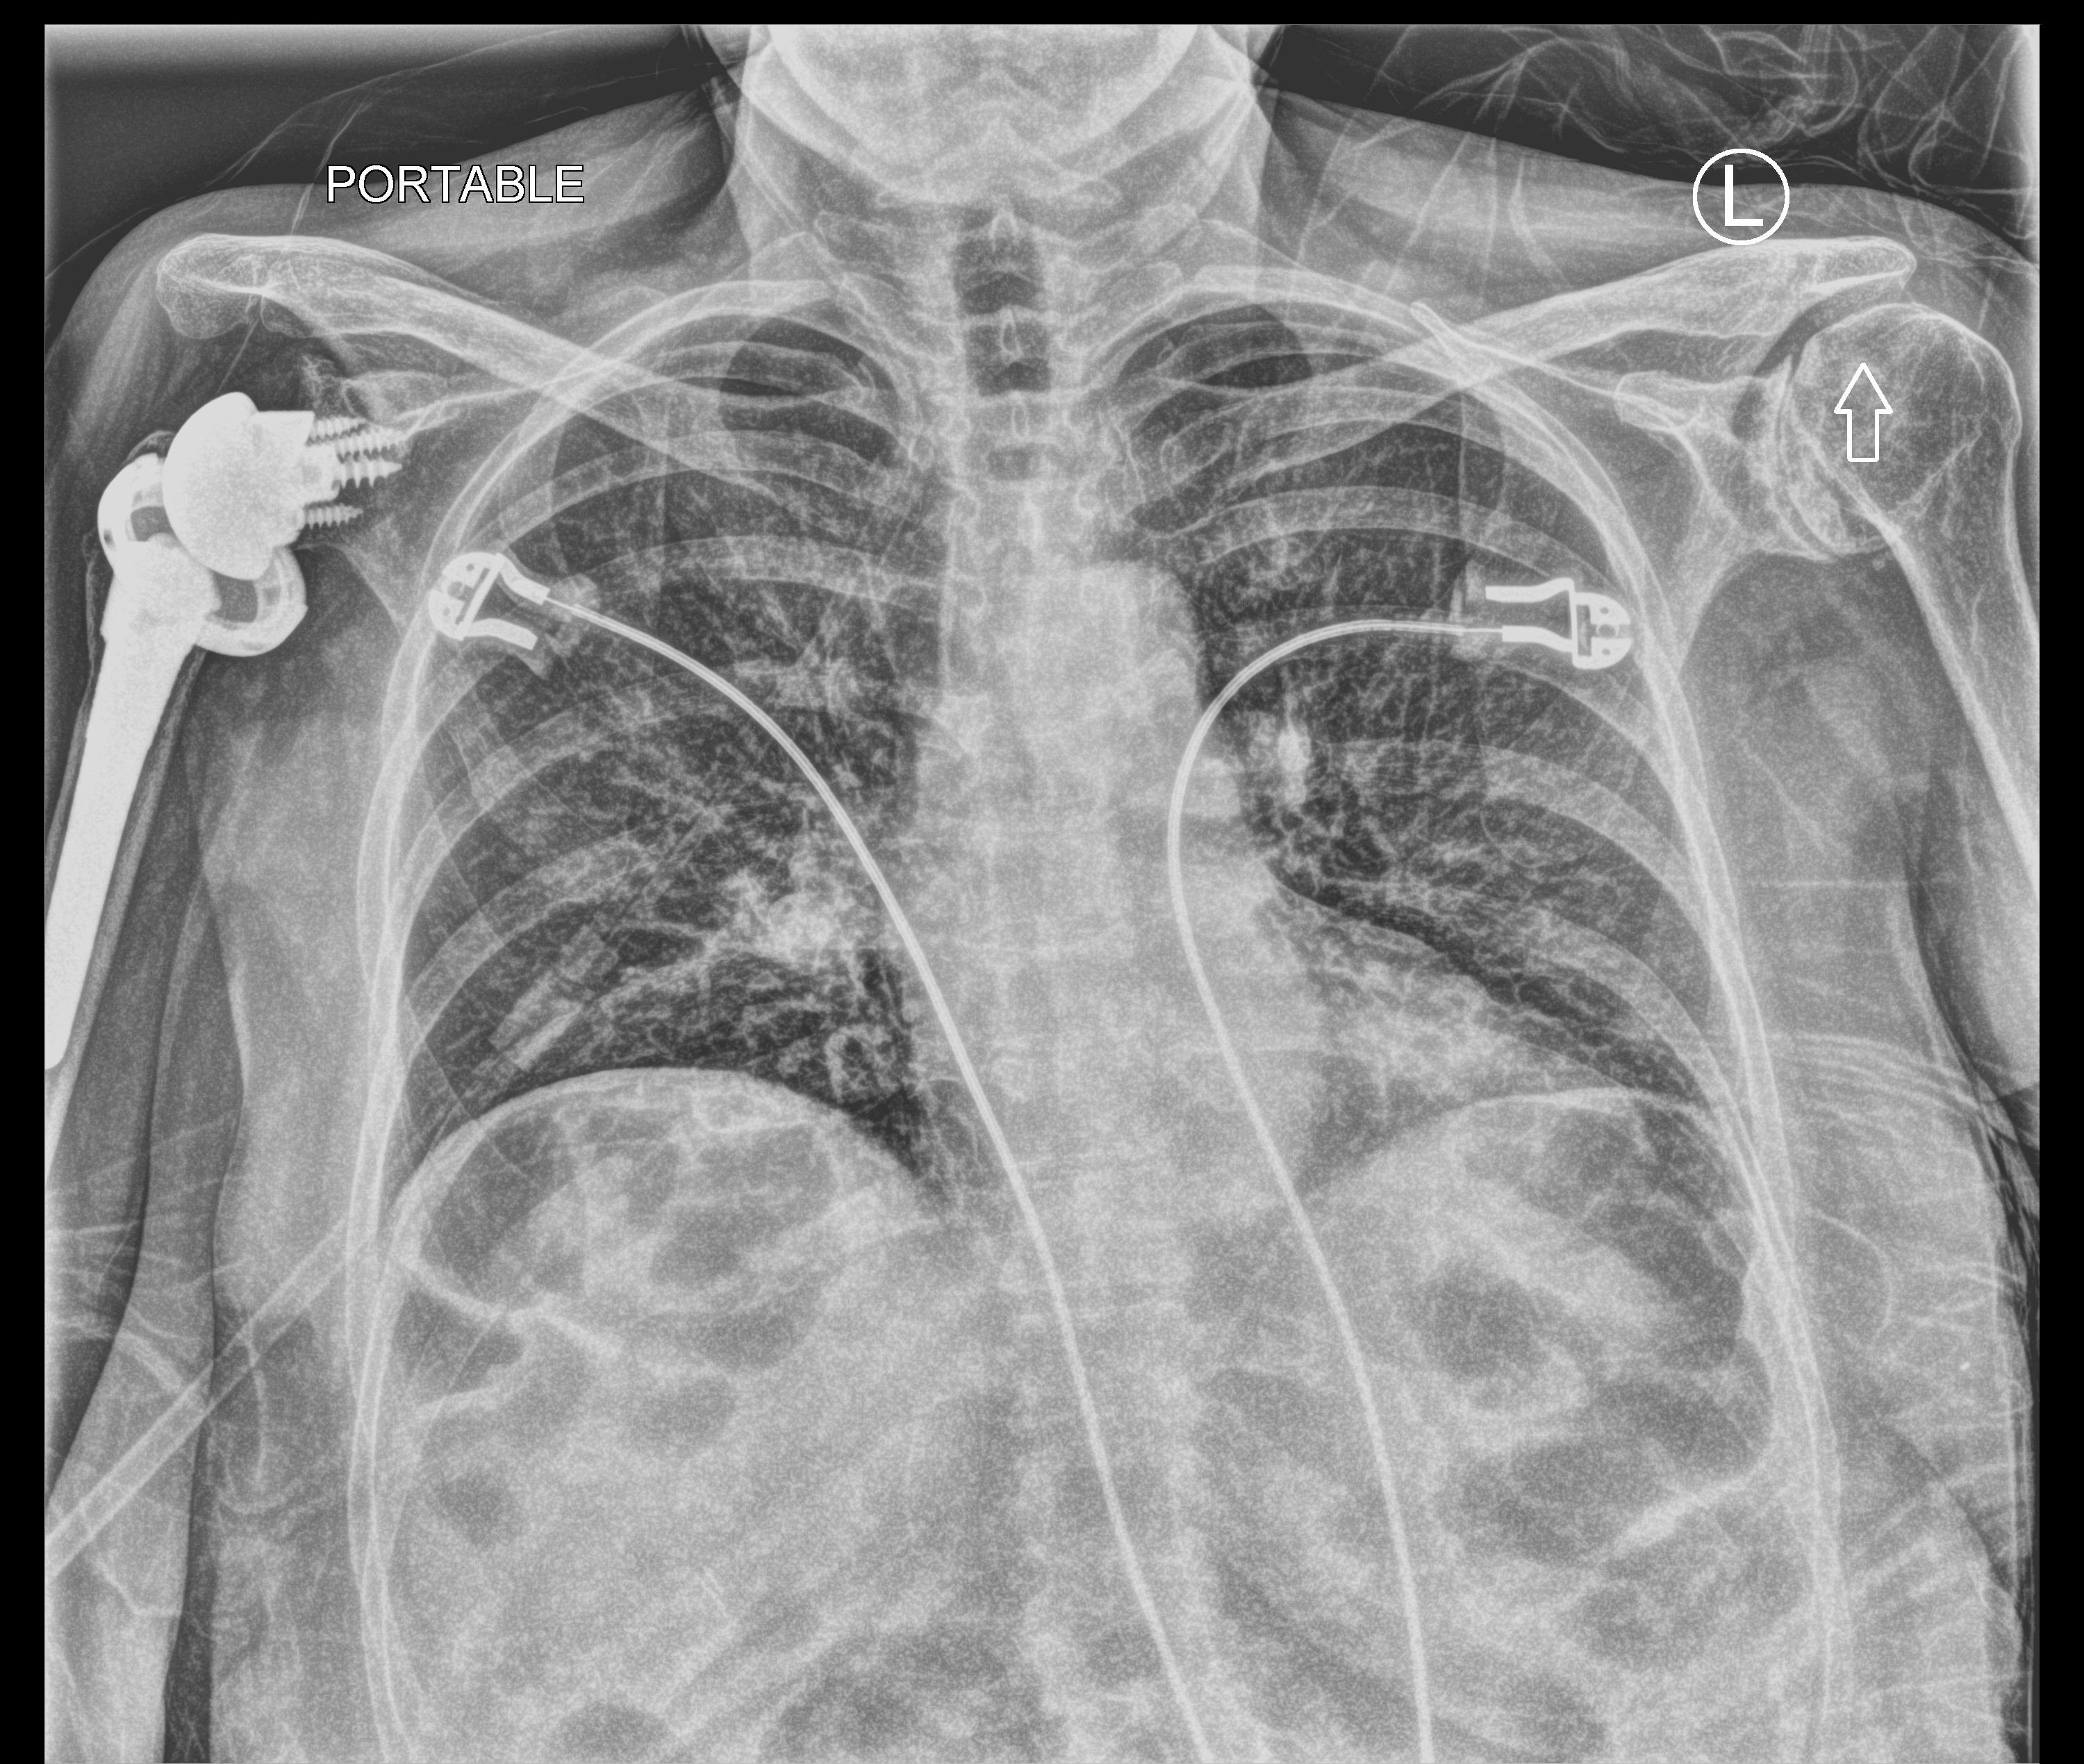
Portable chest radiograph; anteroposterior (AP) projection. Female patient hospitalised with COVID-19, age 60–74 years.
Hospital-stay facts (about this admission, not read from this image; timing relative to this image not recorded):
- admitted to intensive care during this hospital stay: yes